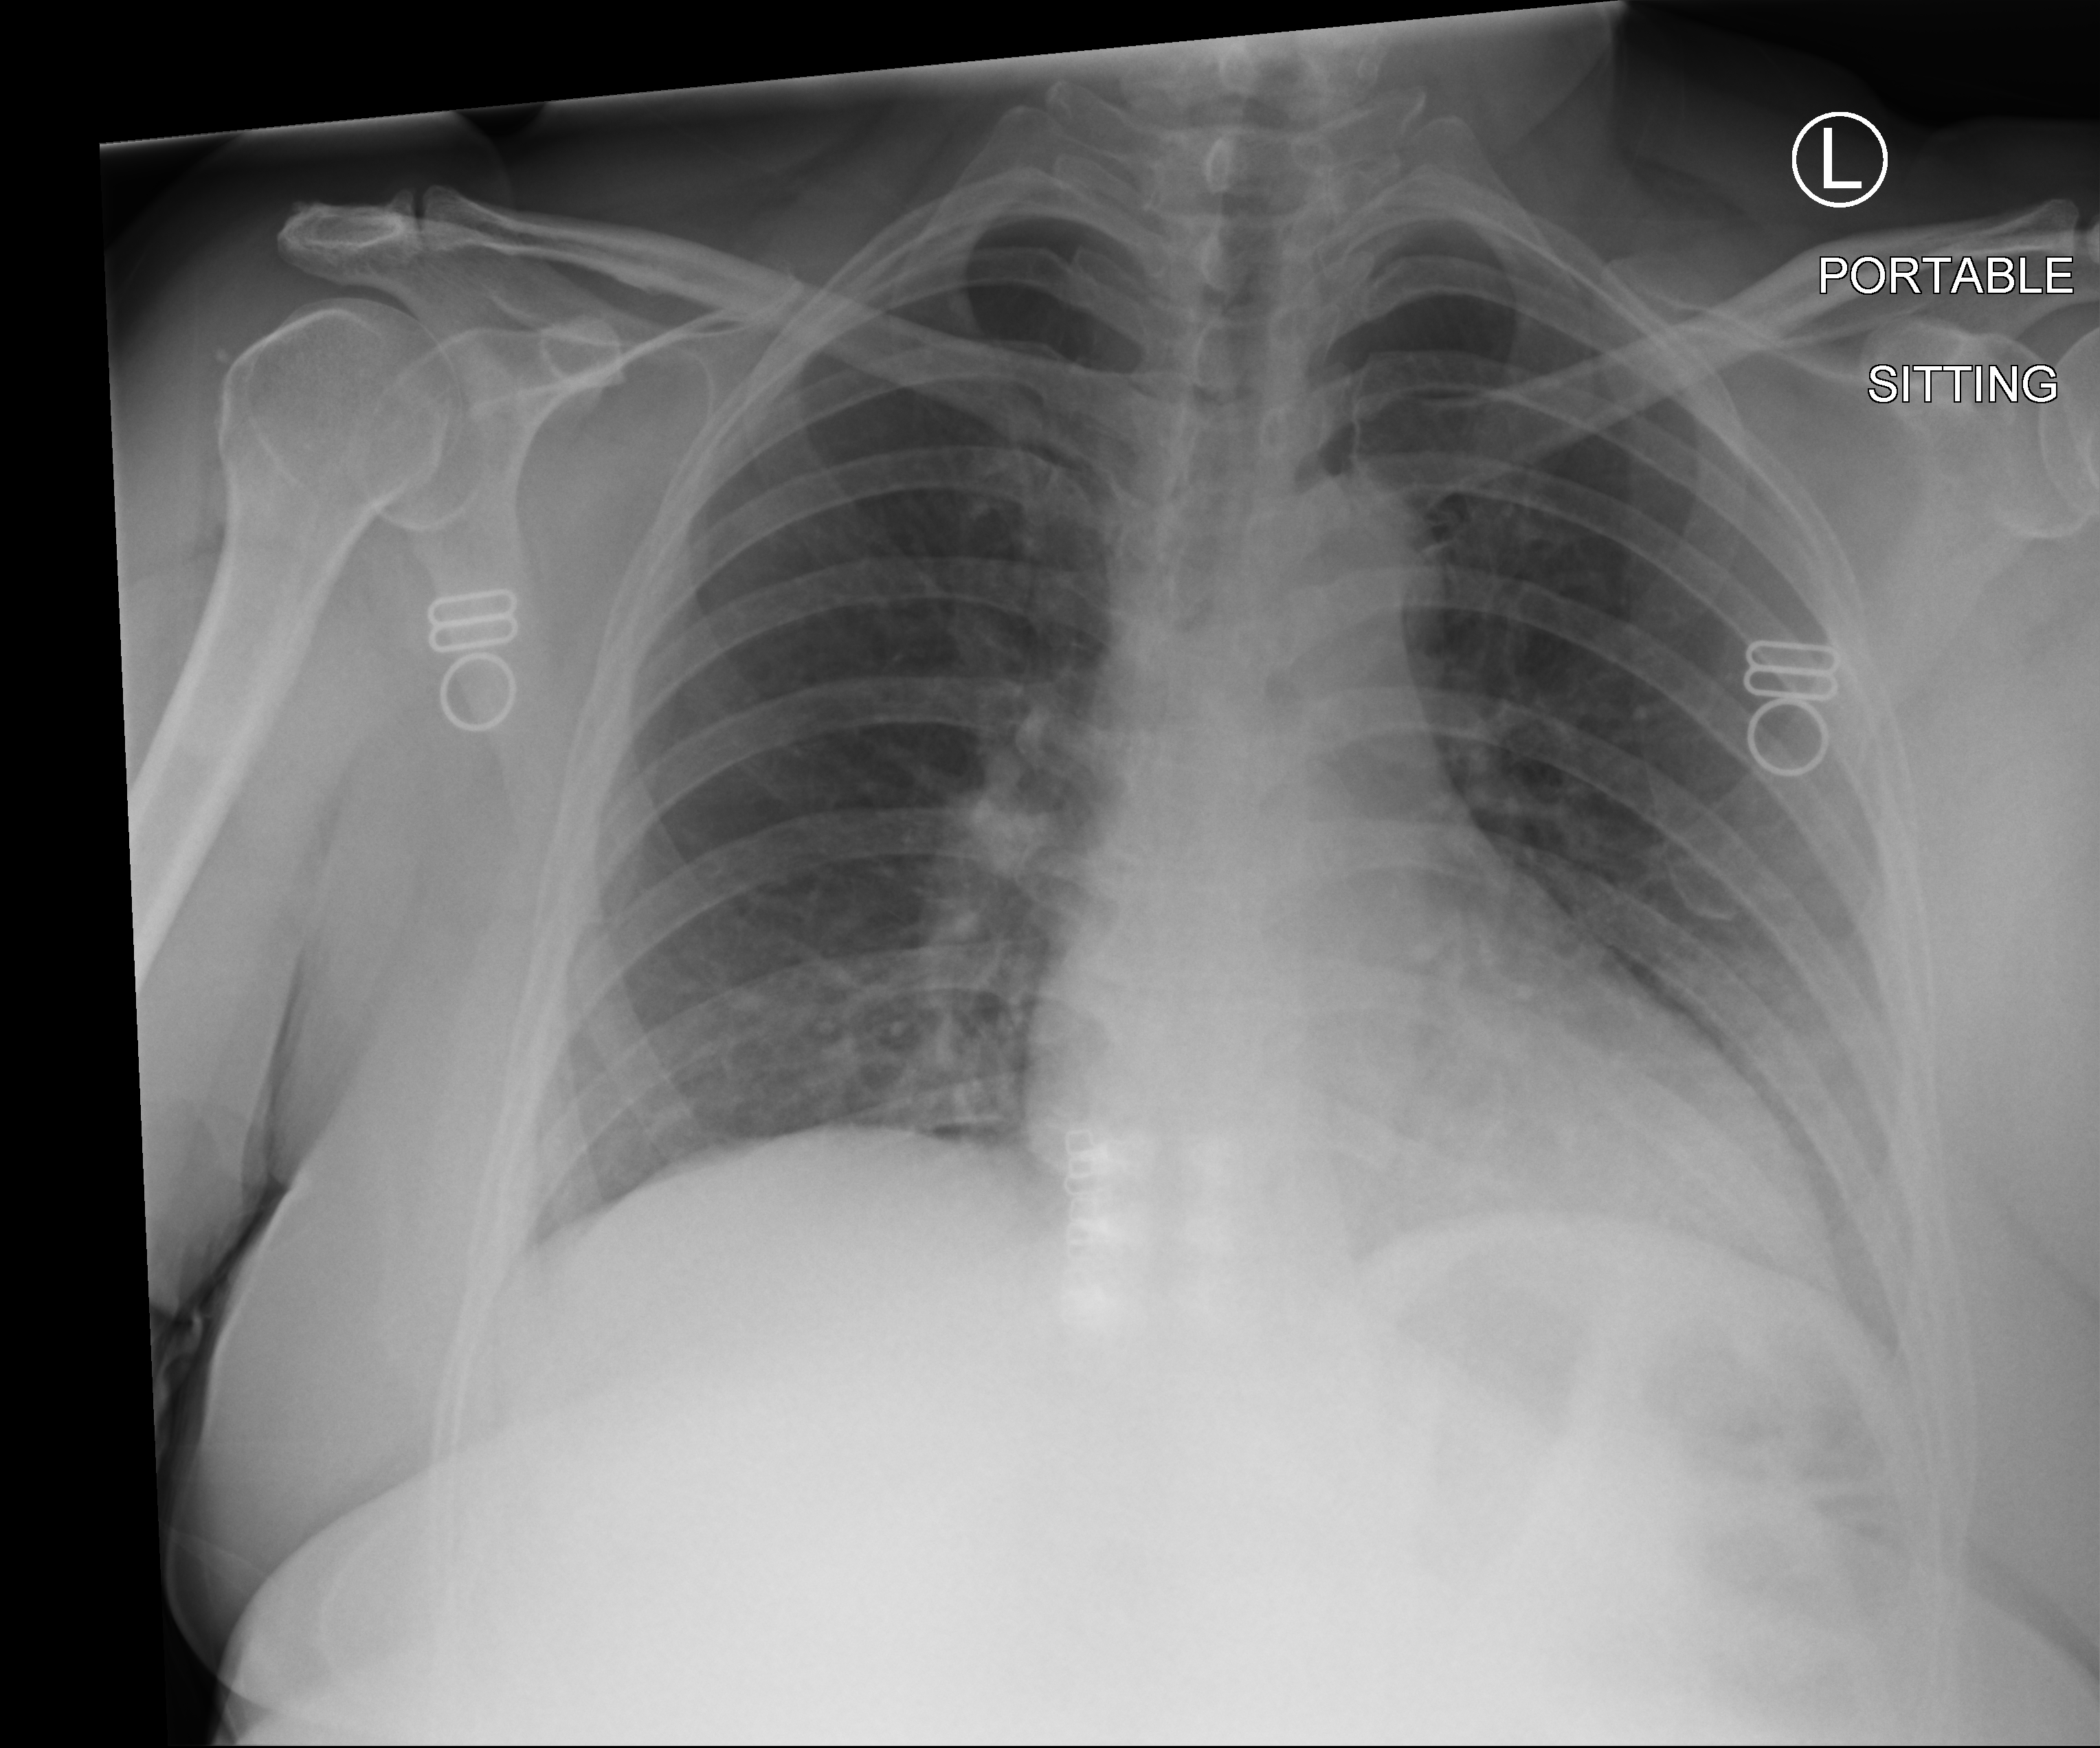
Bedside chest radiograph (computed radiography); anteroposterior (AP) projection. Female patient hospitalised with COVID-19, age 60–74 years.
Hospital-stay facts (about this admission, not read from this image; timing relative to this image not recorded): admitted to intensive care during this hospital stay: no; length of hospital stay: 1 day.